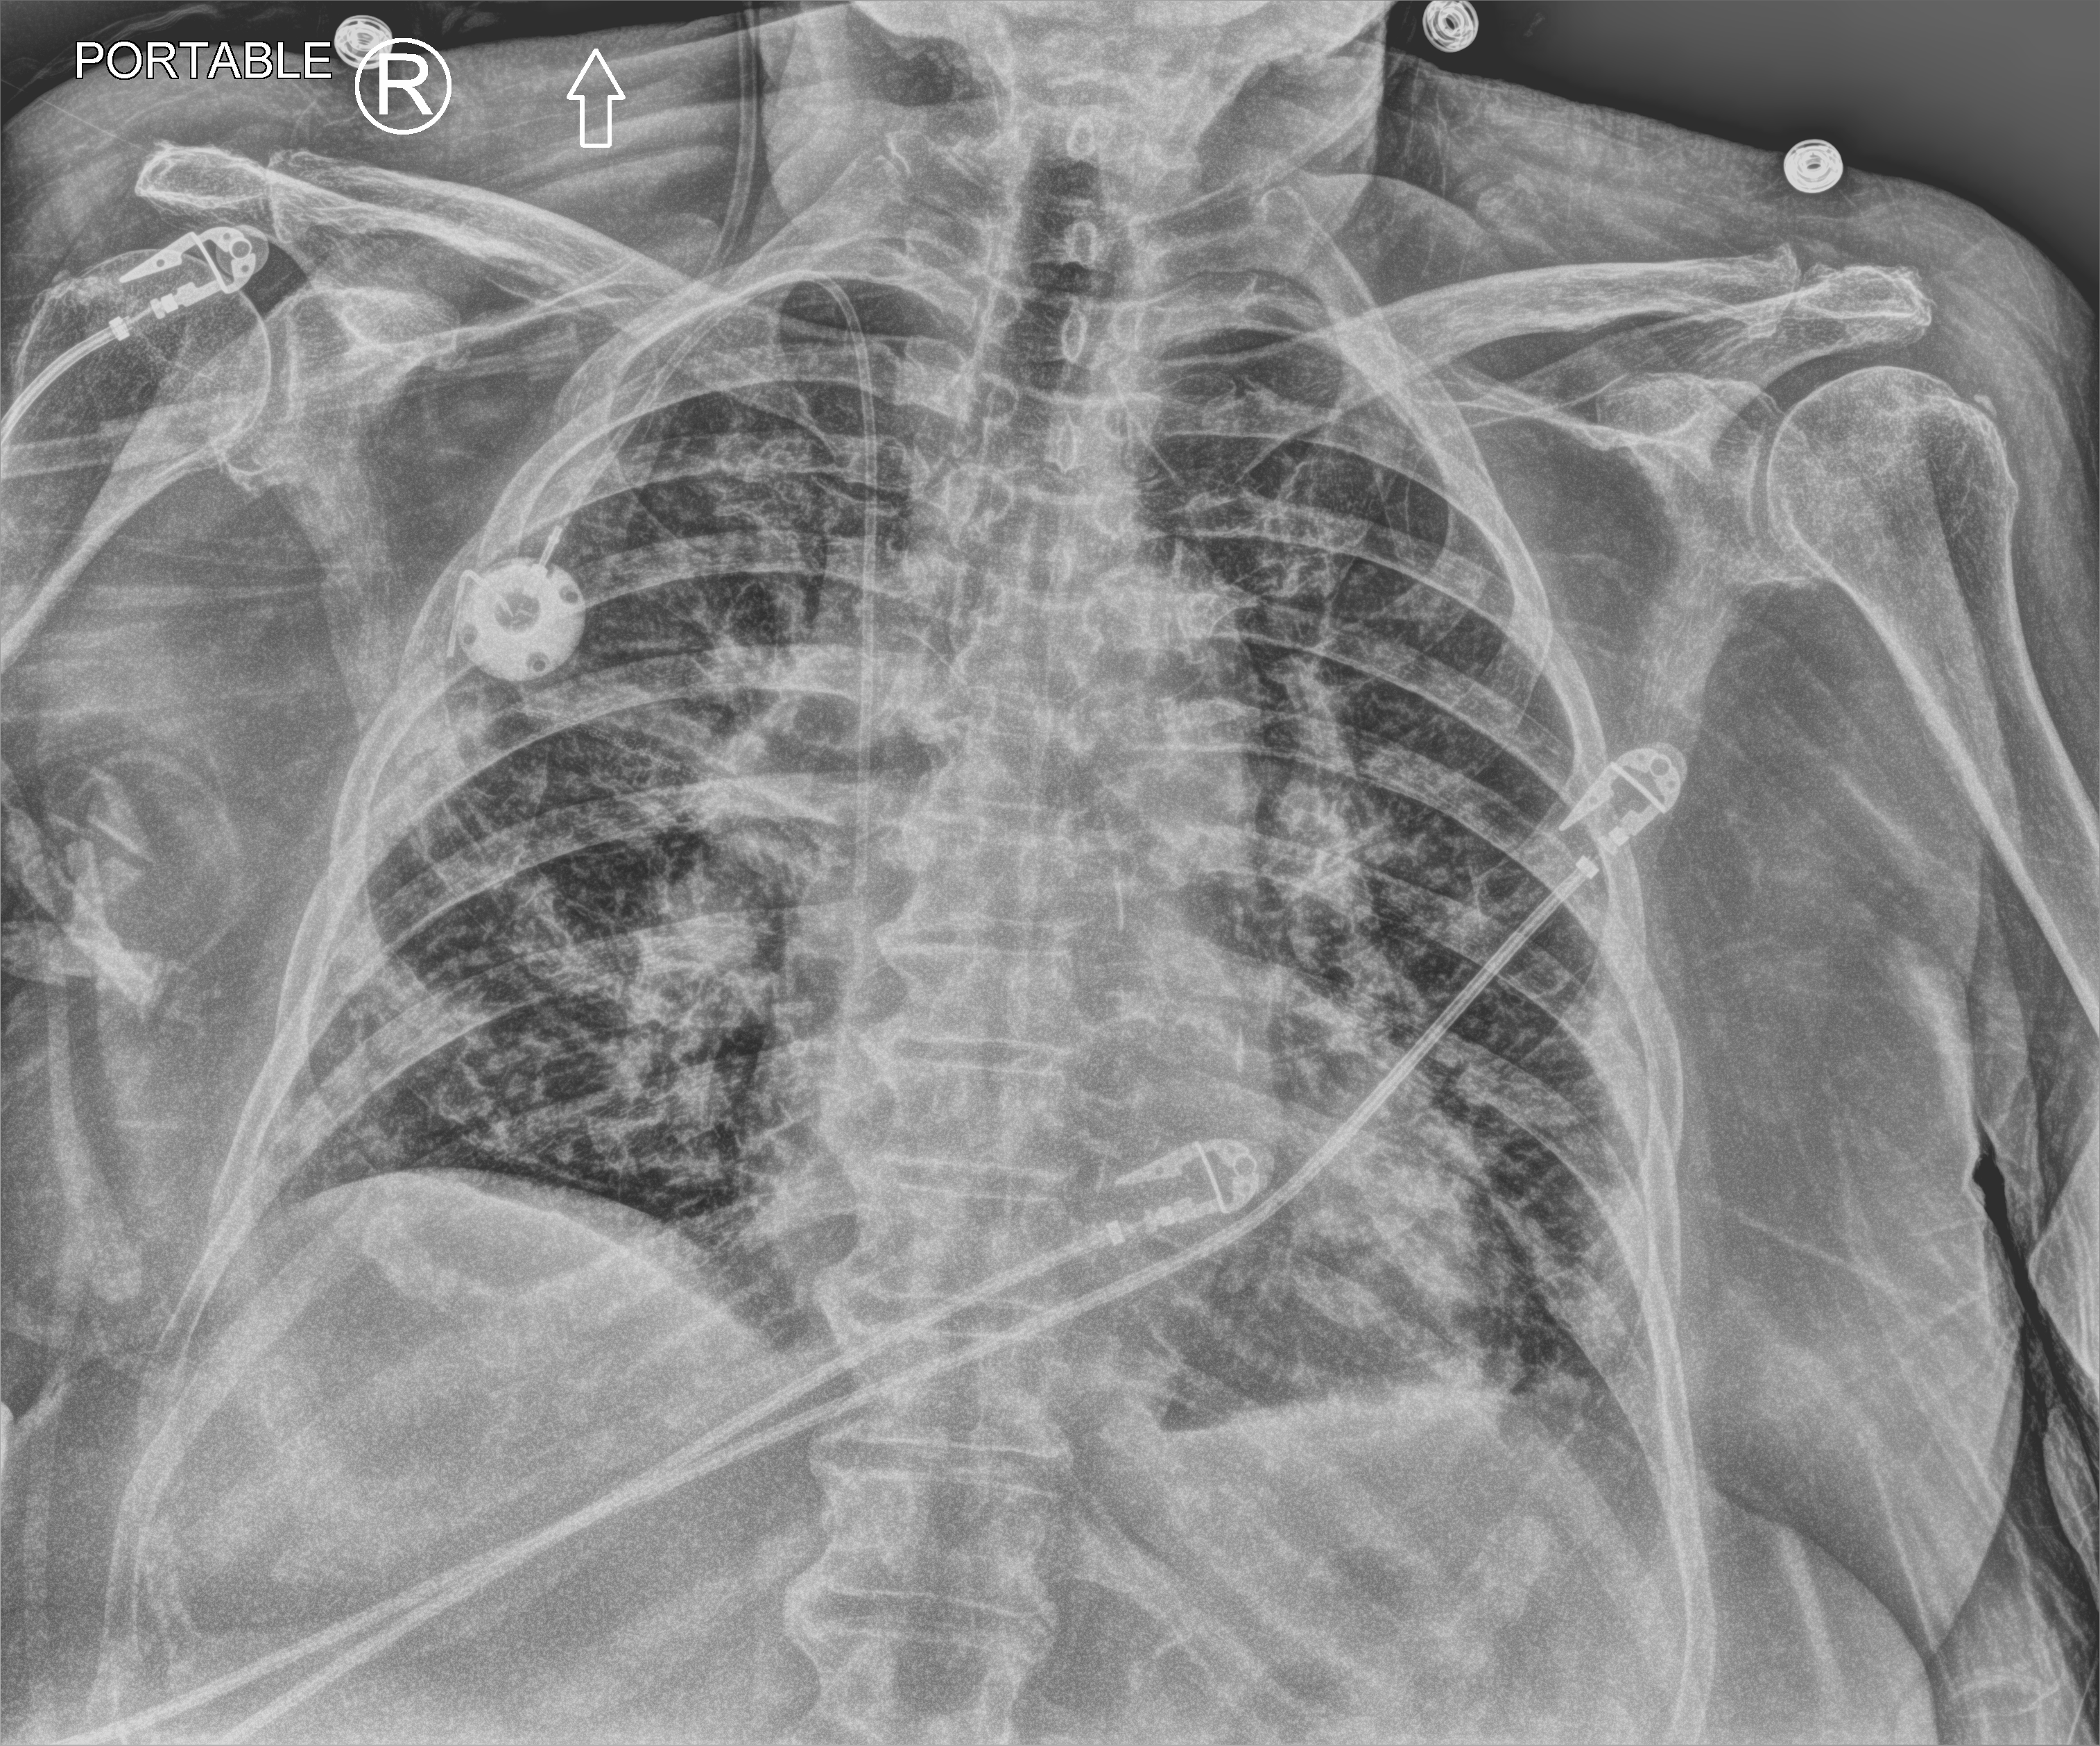
Bedside chest radiograph (computed radiography); anteroposterior (AP) projection. Female patient hospitalised with COVID-19, age 75–90 years.
From the hospital-stay record, not from the radiograph (when in the stay this image was taken is not recorded):
- admitted to intensive care during this hospital stay: no
- mechanically ventilated during this hospital stay: no